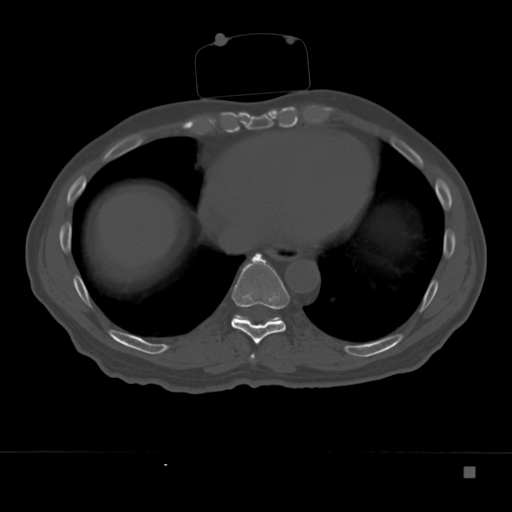
CT including the spine, one axial slice; slice 187 of 332 in the series (ordered by position); bone window (W 1800 / L 400 HU); 1.5 mm slice thickness; 512 × 512 image matrix. Patient: male, 72 years. From the clinical record (not read from this slice): primary cancer: skeletal.
Structures marked on this image (semi-automatically segmented with operator editing):
- T8 vertebra: bounding box (x1, y1, x2, y2) in pixels: (250, 353, 255, 360)
- T9 vertebra: (231, 253, 290, 344)